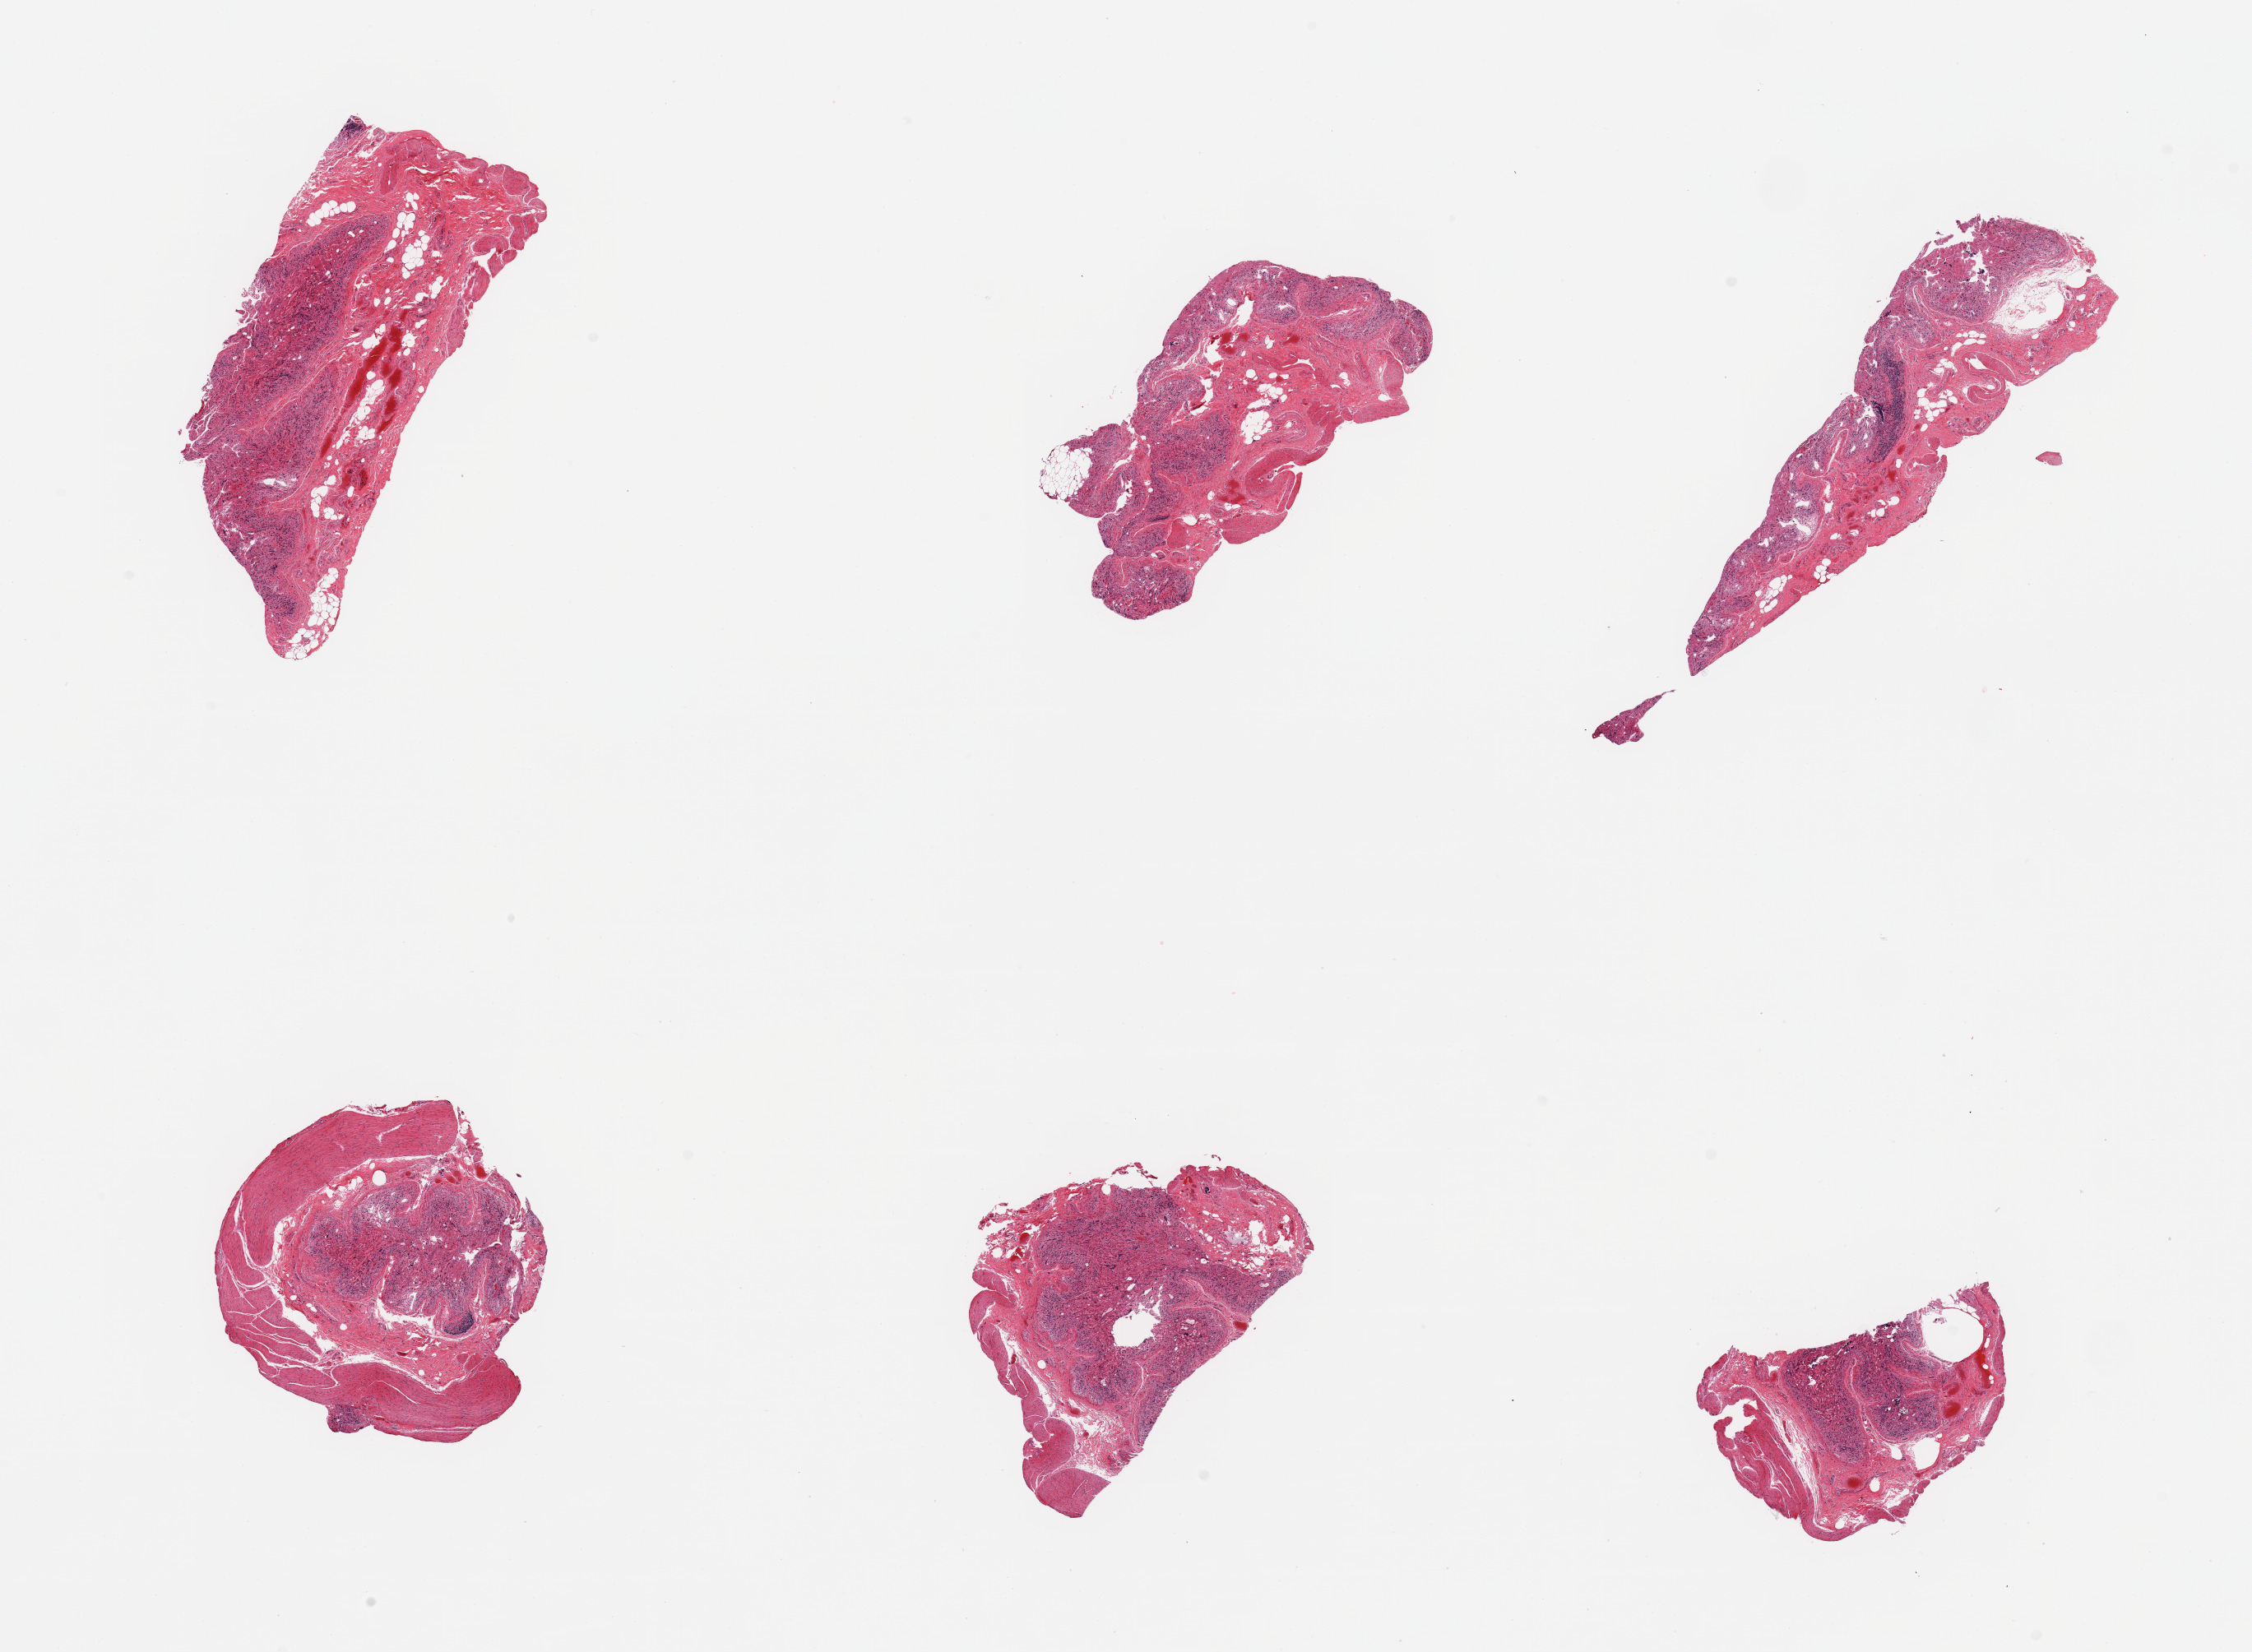
Whole-slide image, hematoxylin and eosin (H&E) stain — a low-resolution overview of the entire scanned area, about 21.7 x 15.9 mm (acquisition: 20x scan), PAXgene-fixed, paraffin-embedded tissue, sampled site (target tissue): ileum, tissue donor sample. Donor: male.
- pathologist's review note for this sample: 6 pieces,; insufficient lymphoid aggregates for analysis in correct target